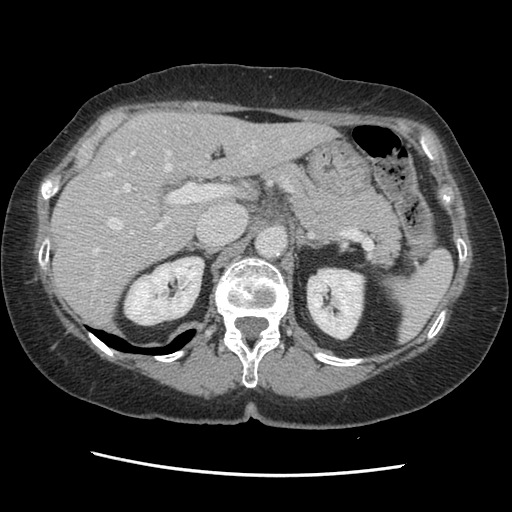
Contrast-enhanced abdominal CT, one axial slice; 120 kVp; soft-tissue window (W 400 / L 40 HU); 2.5 mm slice thickness; 512 × 512 image matrix. Female patient, age 61 years. Case-level facts recorded for this patient, not image findings: diagnosis: colorectal cancer liver metastases, imaged before liver resection; multiple liver metastases: no; largest metastasis: 2.4 cm; chemotherapy before resection: no.
Outlined on this slice (manually delineated by an expert):
- hepatic veins: bounding box (x1, y1, x2, y2) in pixels: (82, 130, 285, 287)
- liver: (52, 112, 335, 329)
- planned liver remnant (the part of the liver to remain after resection): (52, 112, 335, 329)
- portal vein (with intrahepatic branches): (115, 151, 230, 230)